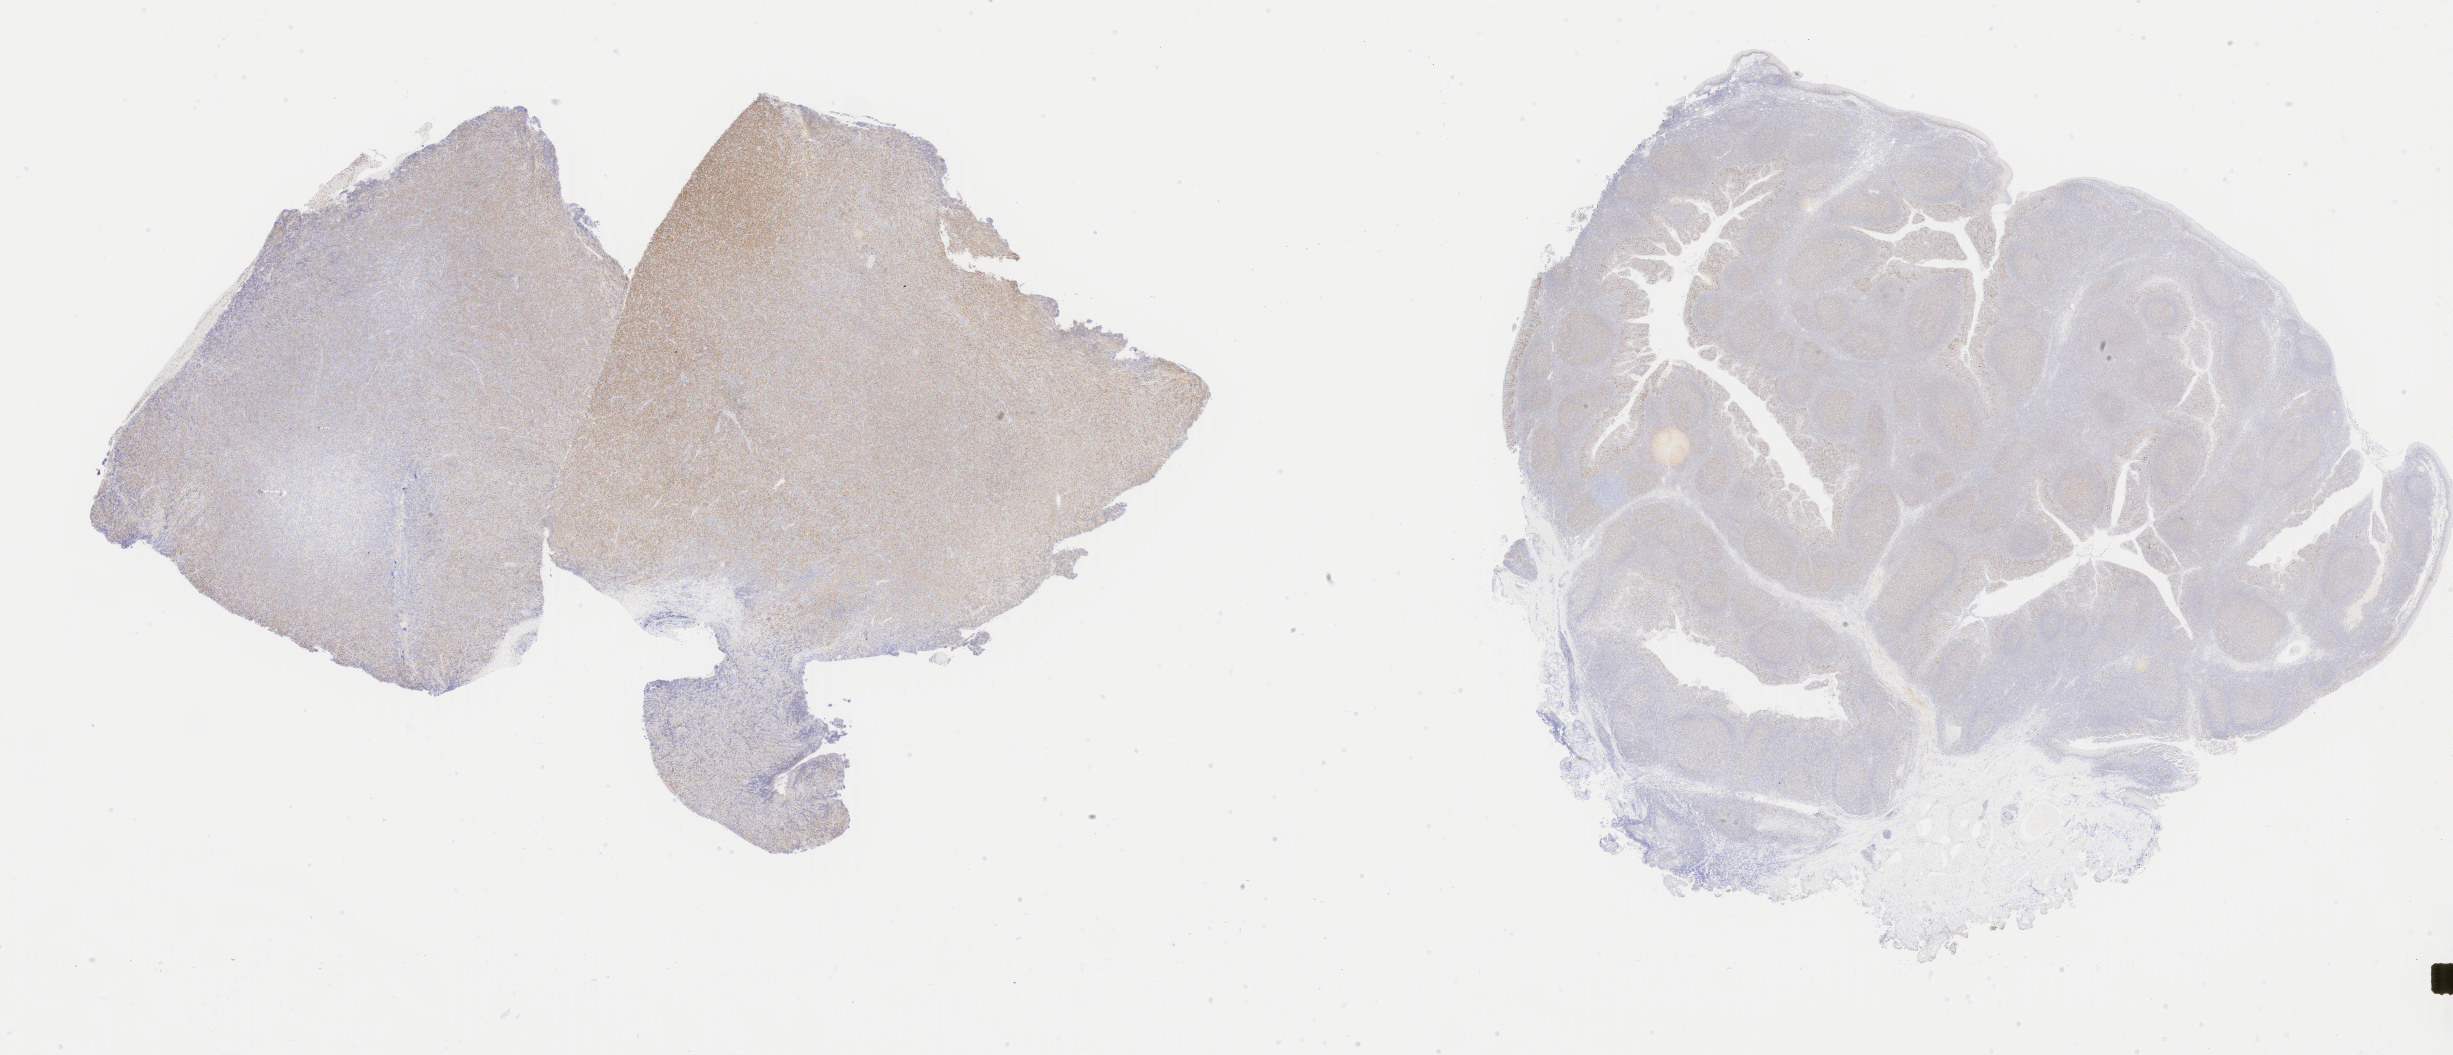
IHC for p53, whole-slide image — low-resolution overview of the scanned area, about 39.0 x 16.8 mm; specimen: tumor tissue. Patient: male, age at initial diagnosis 7 years.
• histologic diagnosis: Diffuse large B-cell lymphoma, NOS